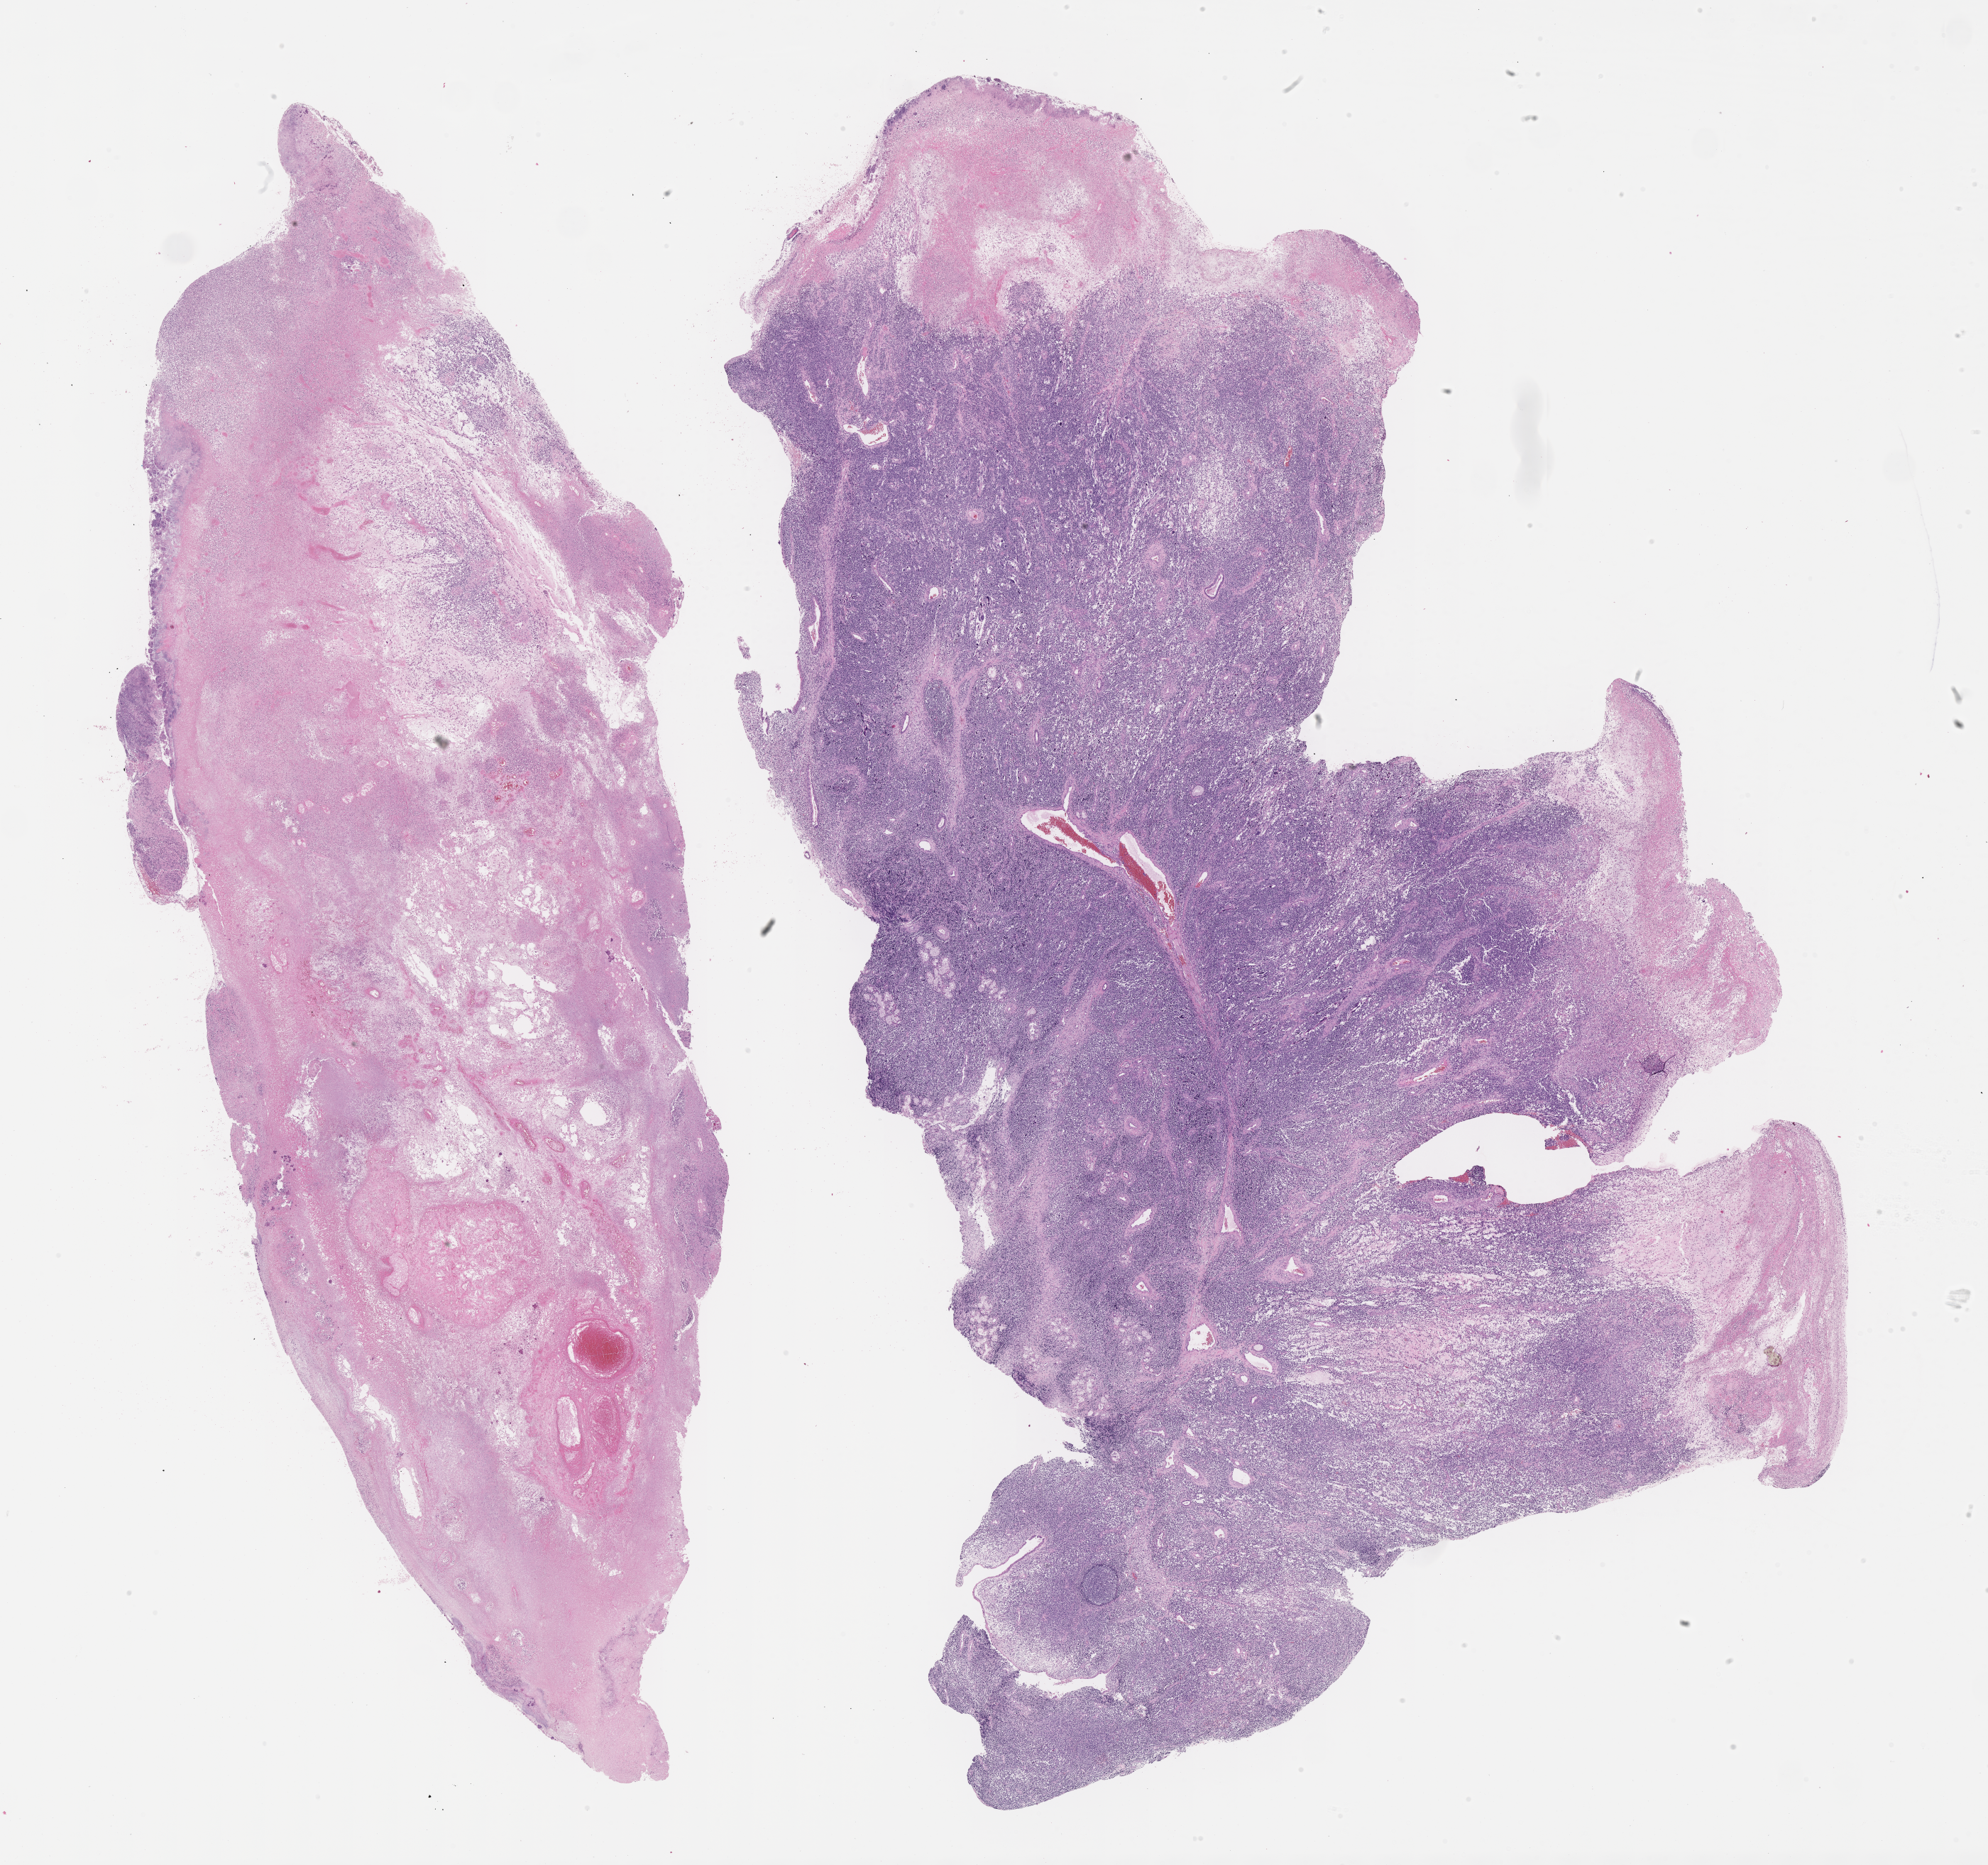
Digitized hematoxylin and eosin (H&E)-stained section of tumor tissue — shown as a low-resolution overview of the whole scanned area (about 22.6 x 21.2 mm). Formalin-fixed paraffin-embedded section. Sample anatomic site: nasopharynx. Patient: female, age 4.5 years at diagnosis.
Diagnosis: rhabdomyosarcoma; histological classification: embryonal rhabdomyosarcoma. Metastatic status at presentation (as recorded): metastatic (confirmed). Stage (as recorded): 4.